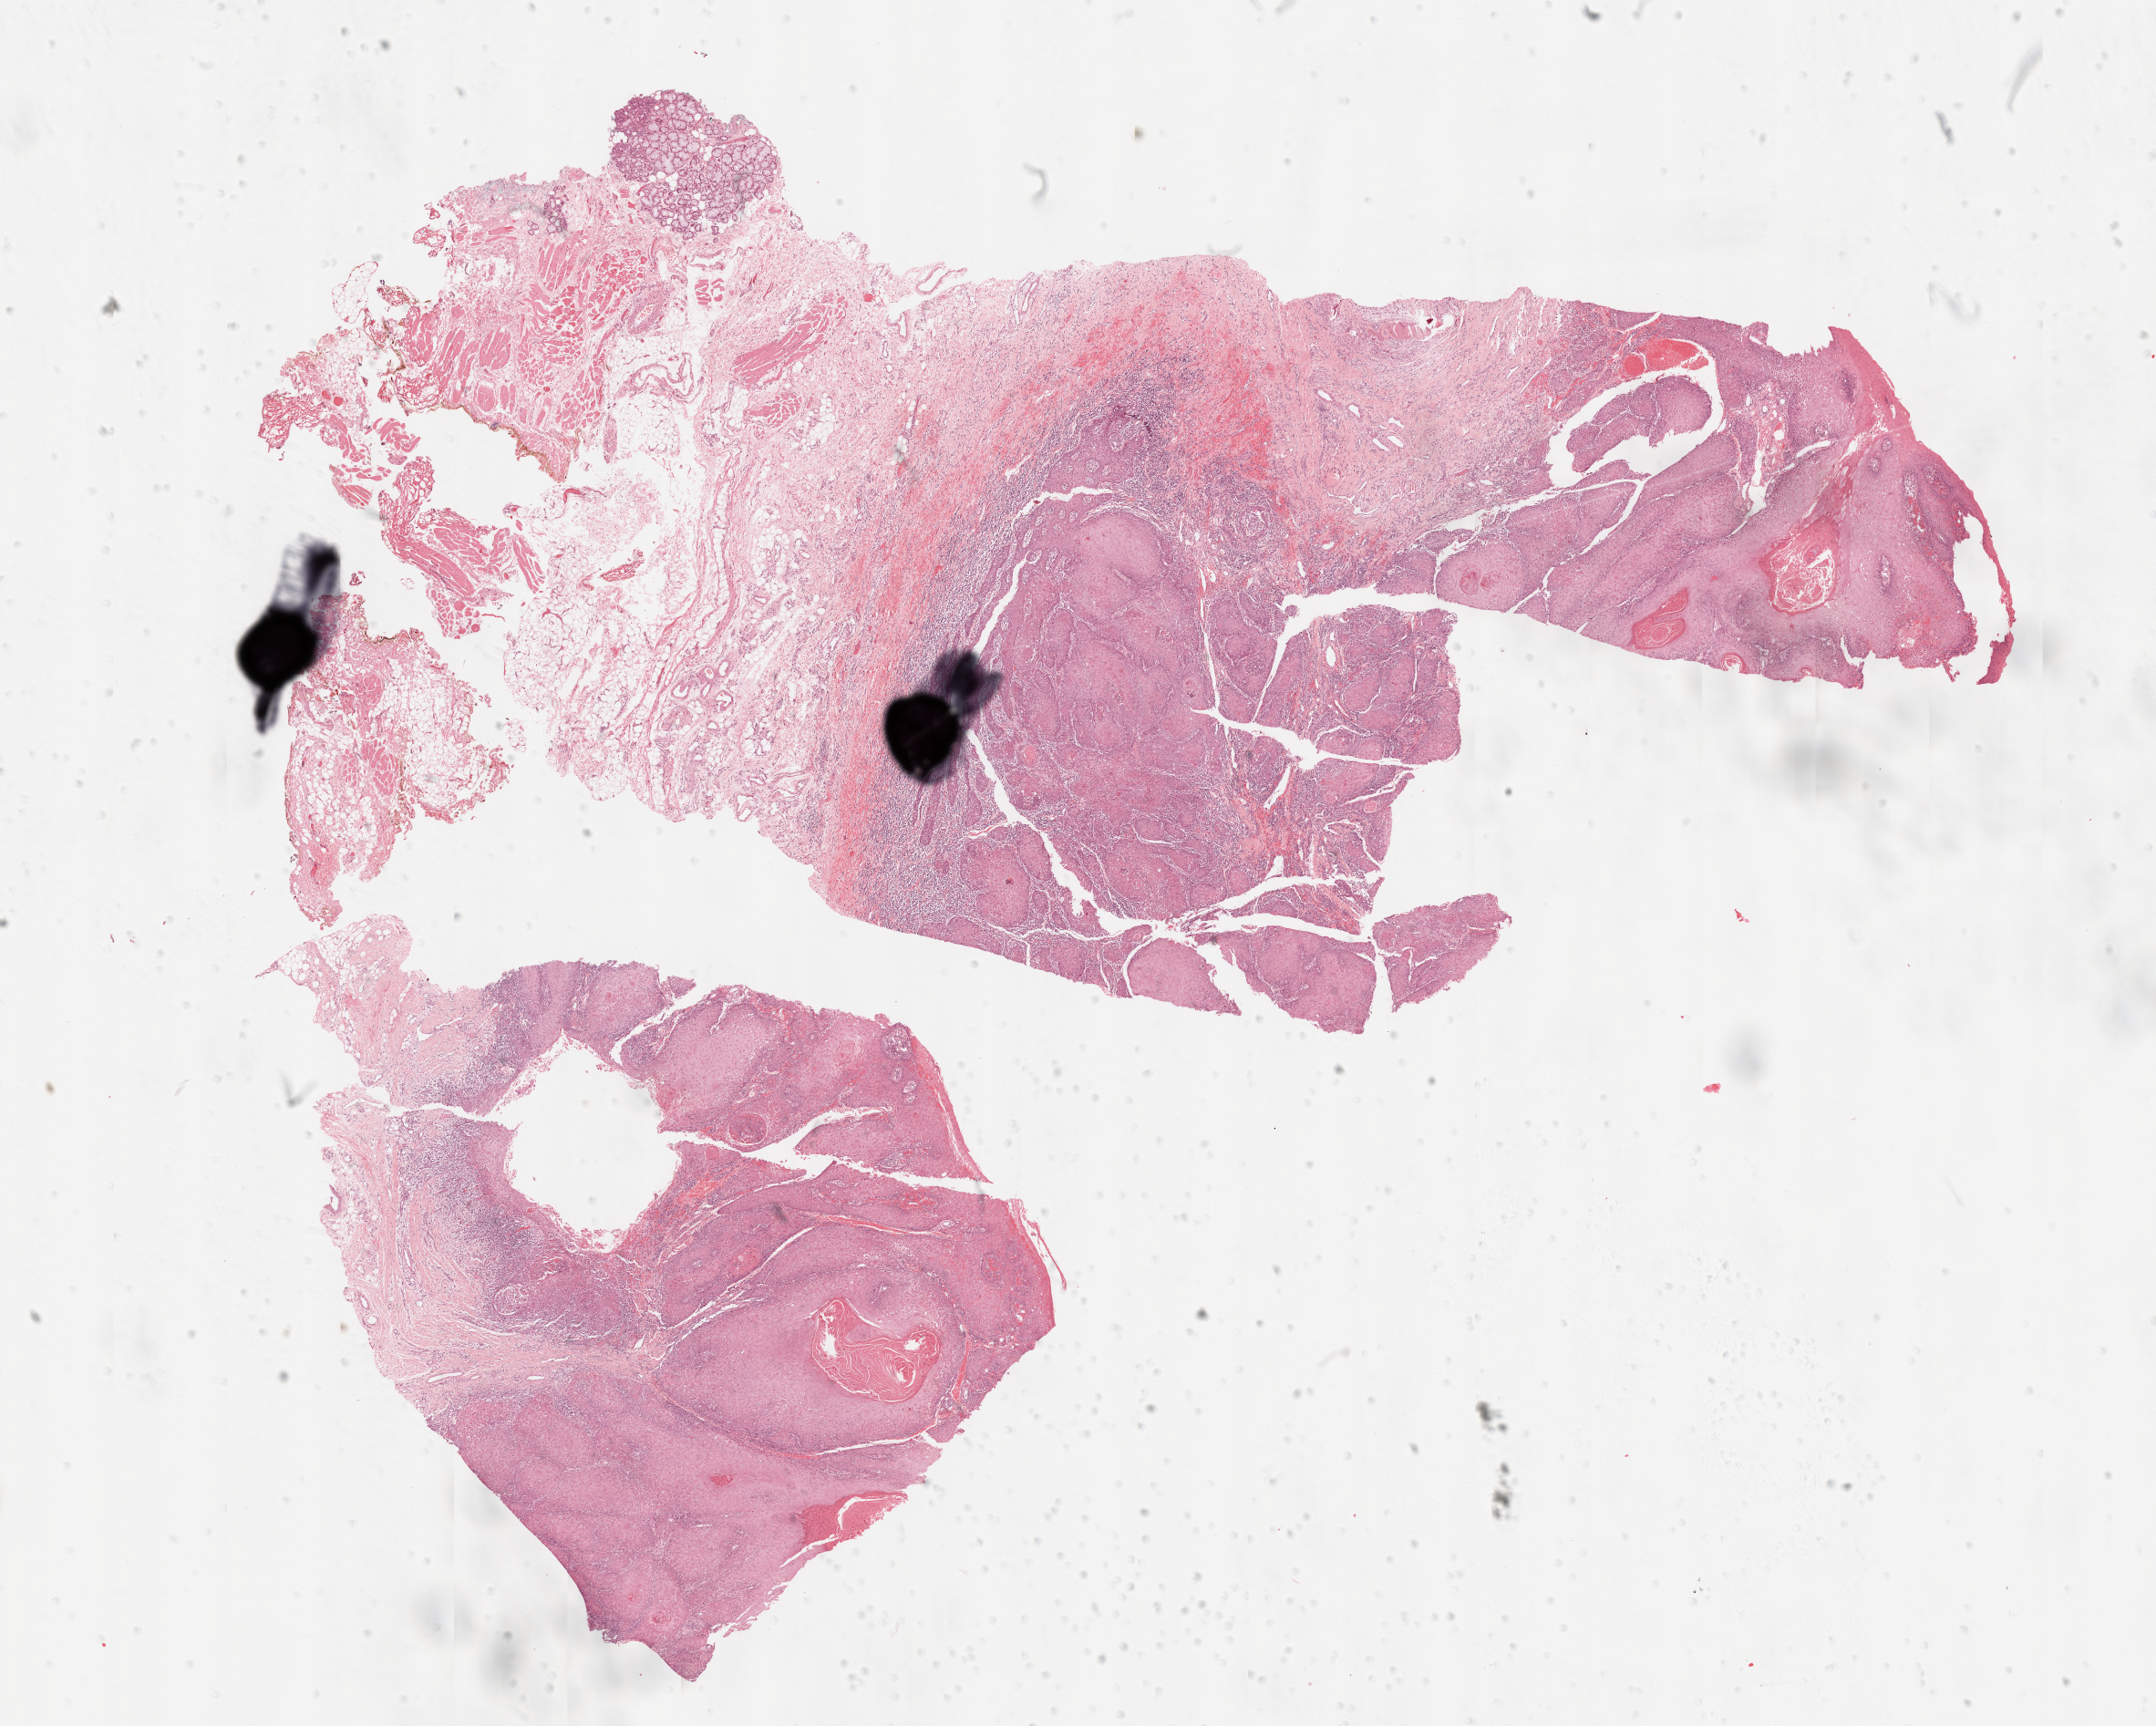
Whole-slide histology image, Hematoxylin and eosin (H&E) stained — whole scanned area (about 19.0 x 15.2 mm) shown as a low-resolution overview; formalin-fixed paraffin-embedded (FFPE) diagnostic section; primary tumour sample from the head and neck. Patient: female, age at initial diagnosis 59 years. Histologic grade: G1 (well differentiated).
Laterality: right. AJCC pathologic stage: I (6th edition). Diagnosis: Squamous cell carcinoma, NOS (mouth, NOS). TNM: T1 NX M0.